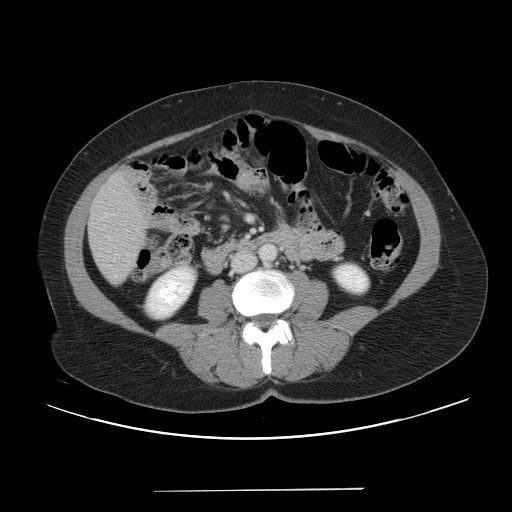
Contrast-enhanced abdominal CT, one axial slice; slice 8 of 56 in the series (ordered by position); 120 kVp; intravenous contrast given; soft-tissue window (W 400 / L 40 HU); 512 × 512 image matrix, field of view 419 × 419 mm. Female patient, age 54 years. From the clinical record (not read from this slice): diagnosis: colorectal cancer liver metastases, imaged before liver resection; multiple liver metastases: yes; largest metastasis: 3.2 cm.
Structures marked on this image (expert manual segmentation):
- liver: box from (x=89, y=173) to (x=147, y=283) px